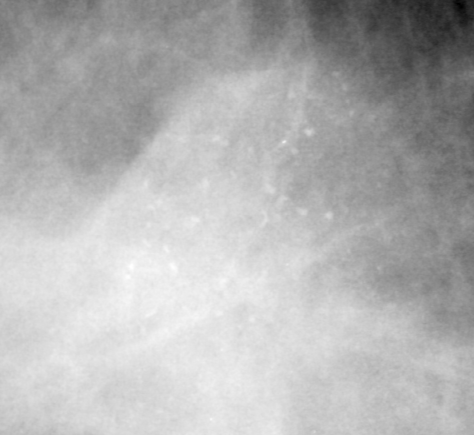
Crop from a digitized film mammogram around one marked abnormality; right breast; CC view.
- Finding: mass, shape irregular, margins spiculated; BI-RADS assessment category 5; subtlety rating 4 on a 1 (subtle) to 5 (obvious) scale; pathology result (as recorded, not read from the image): malignant.